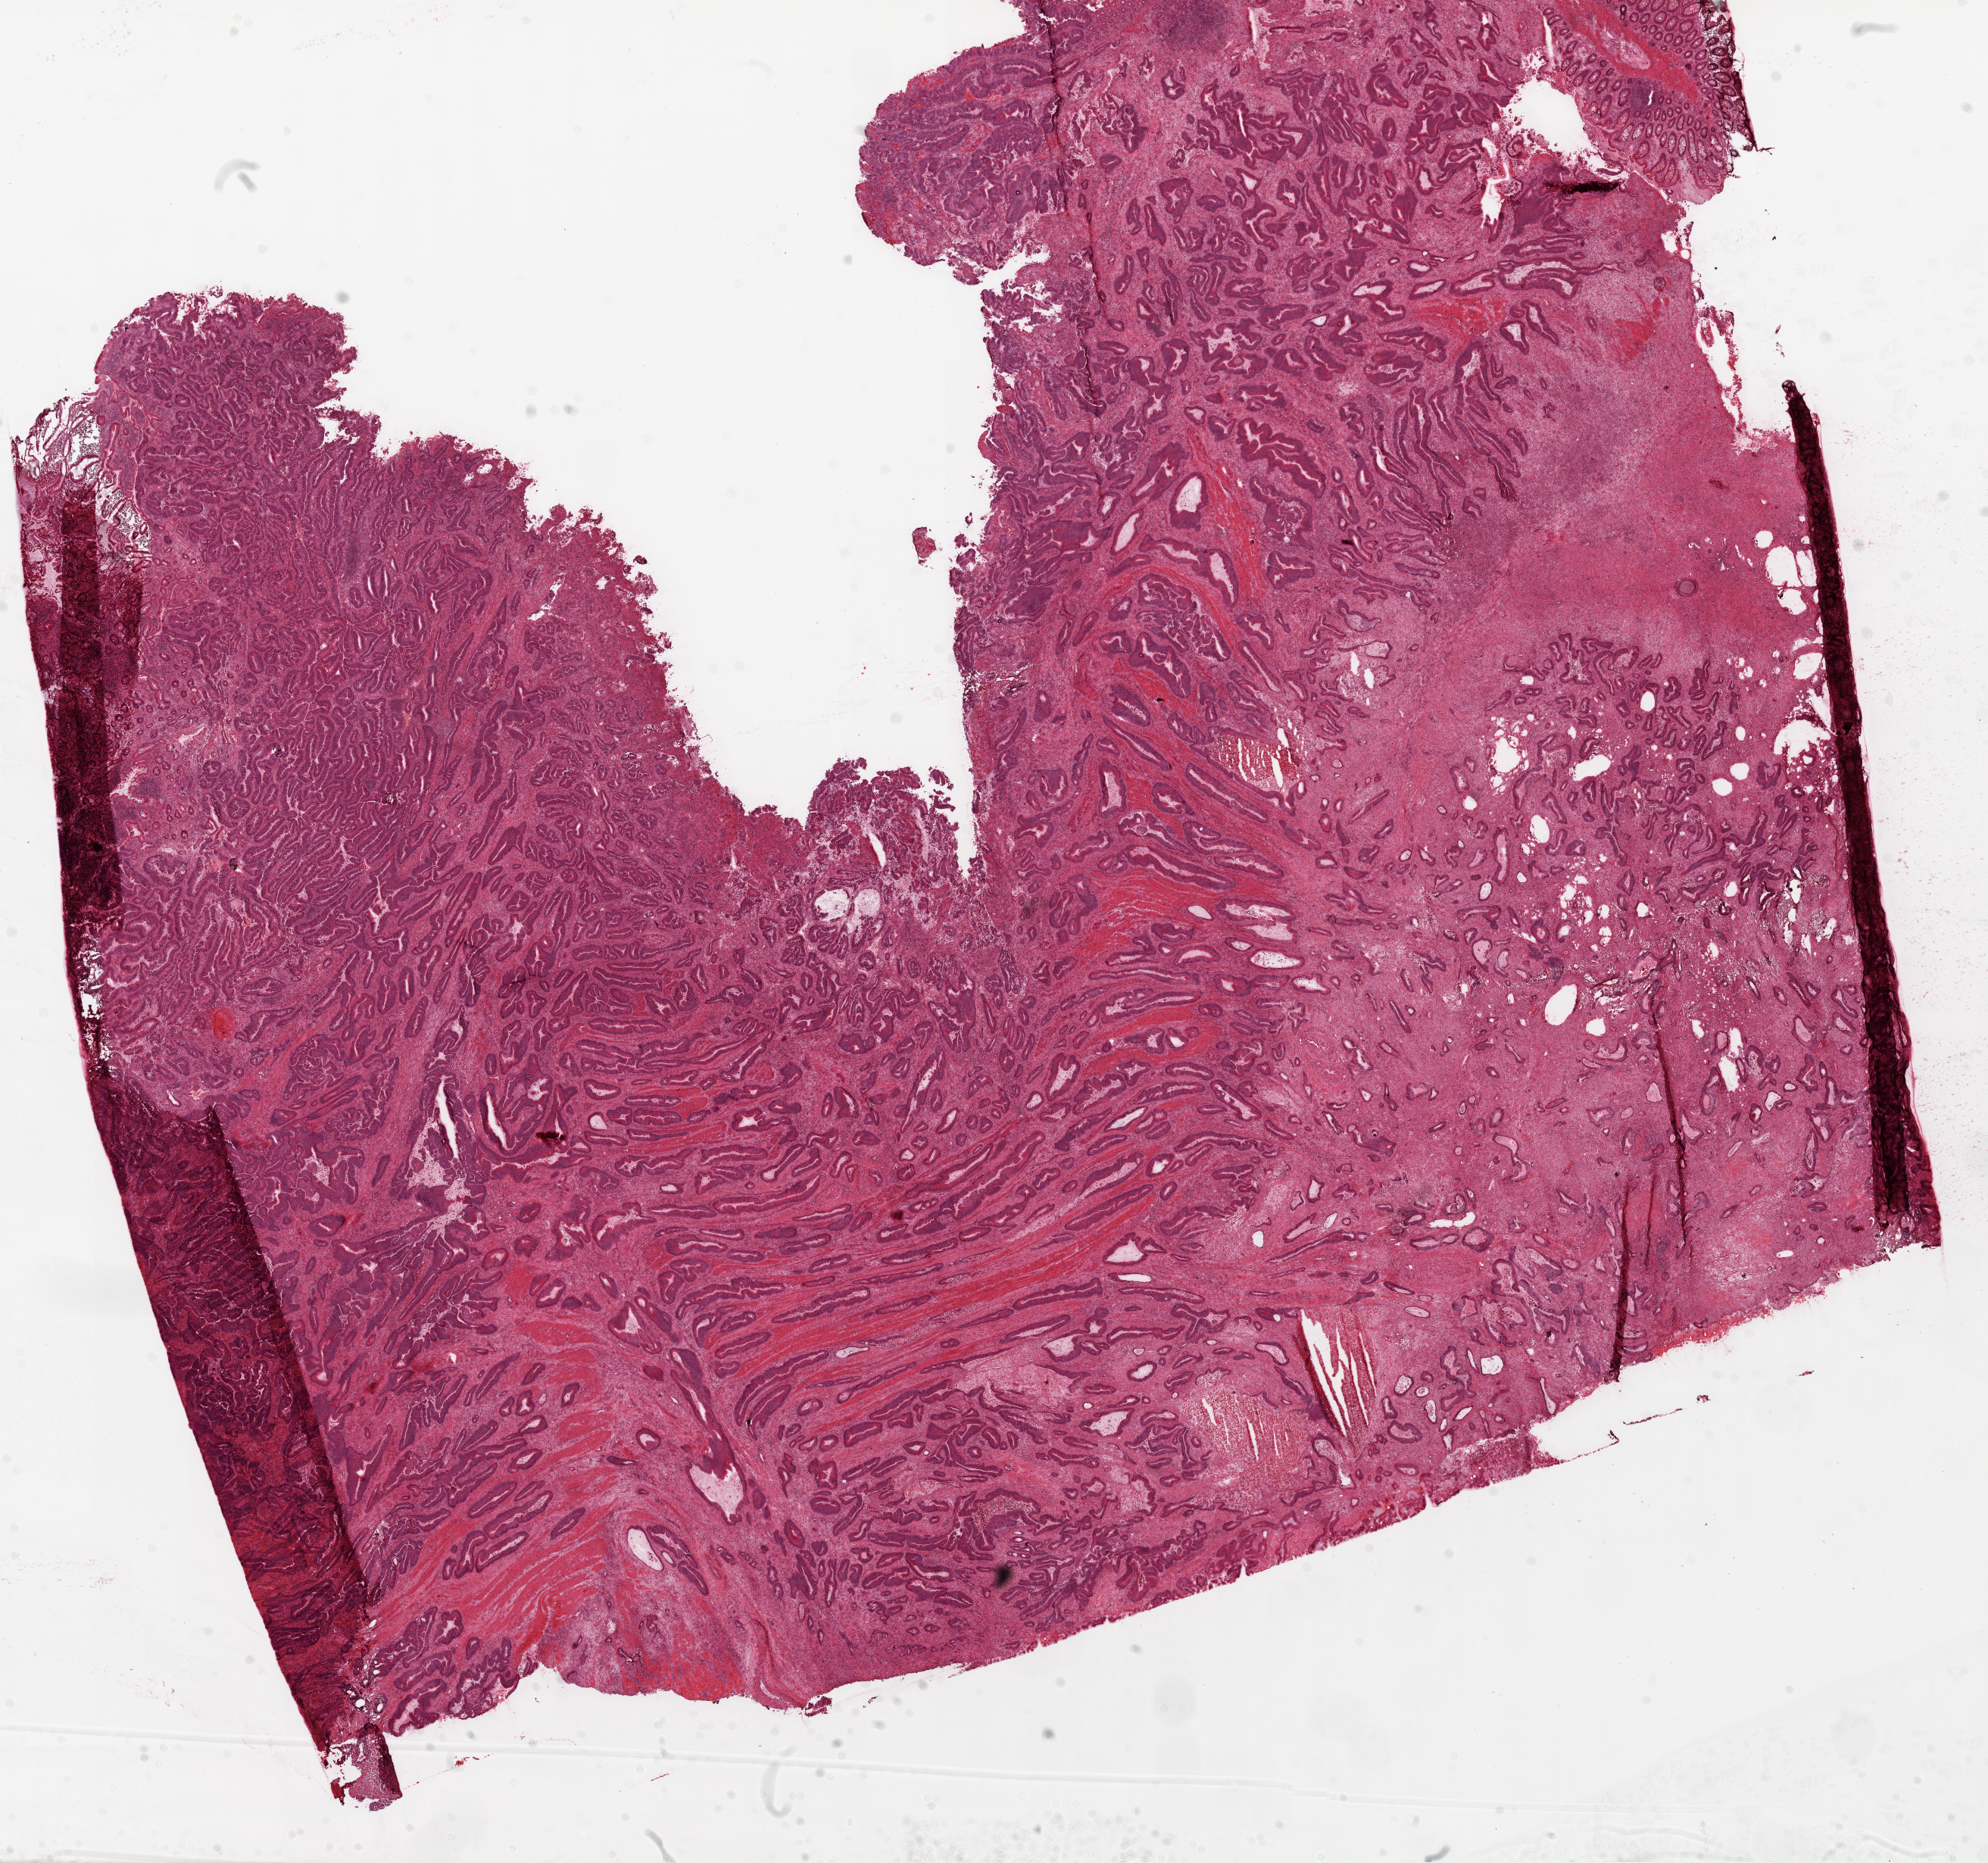
Whole-slide histology image, H&E — whole scanned area (about 21.1 x 19.7 mm) shown as a low-resolution overview; frozen section; sample: primary tumour, colon. Male, age 47 years at initial diagnosis. Pathologist review of this section (percent, as recorded): tumour cells 77%, tumour nuclei 75%, normal cells 5%, stromal cells 15%, necrosis 3%.
AJCC pathologic stage: IVA. Lymph nodes positive (case pathology): 2 of 29 examined. Diagnosis: Adenocarcinoma, NOS (cecum).